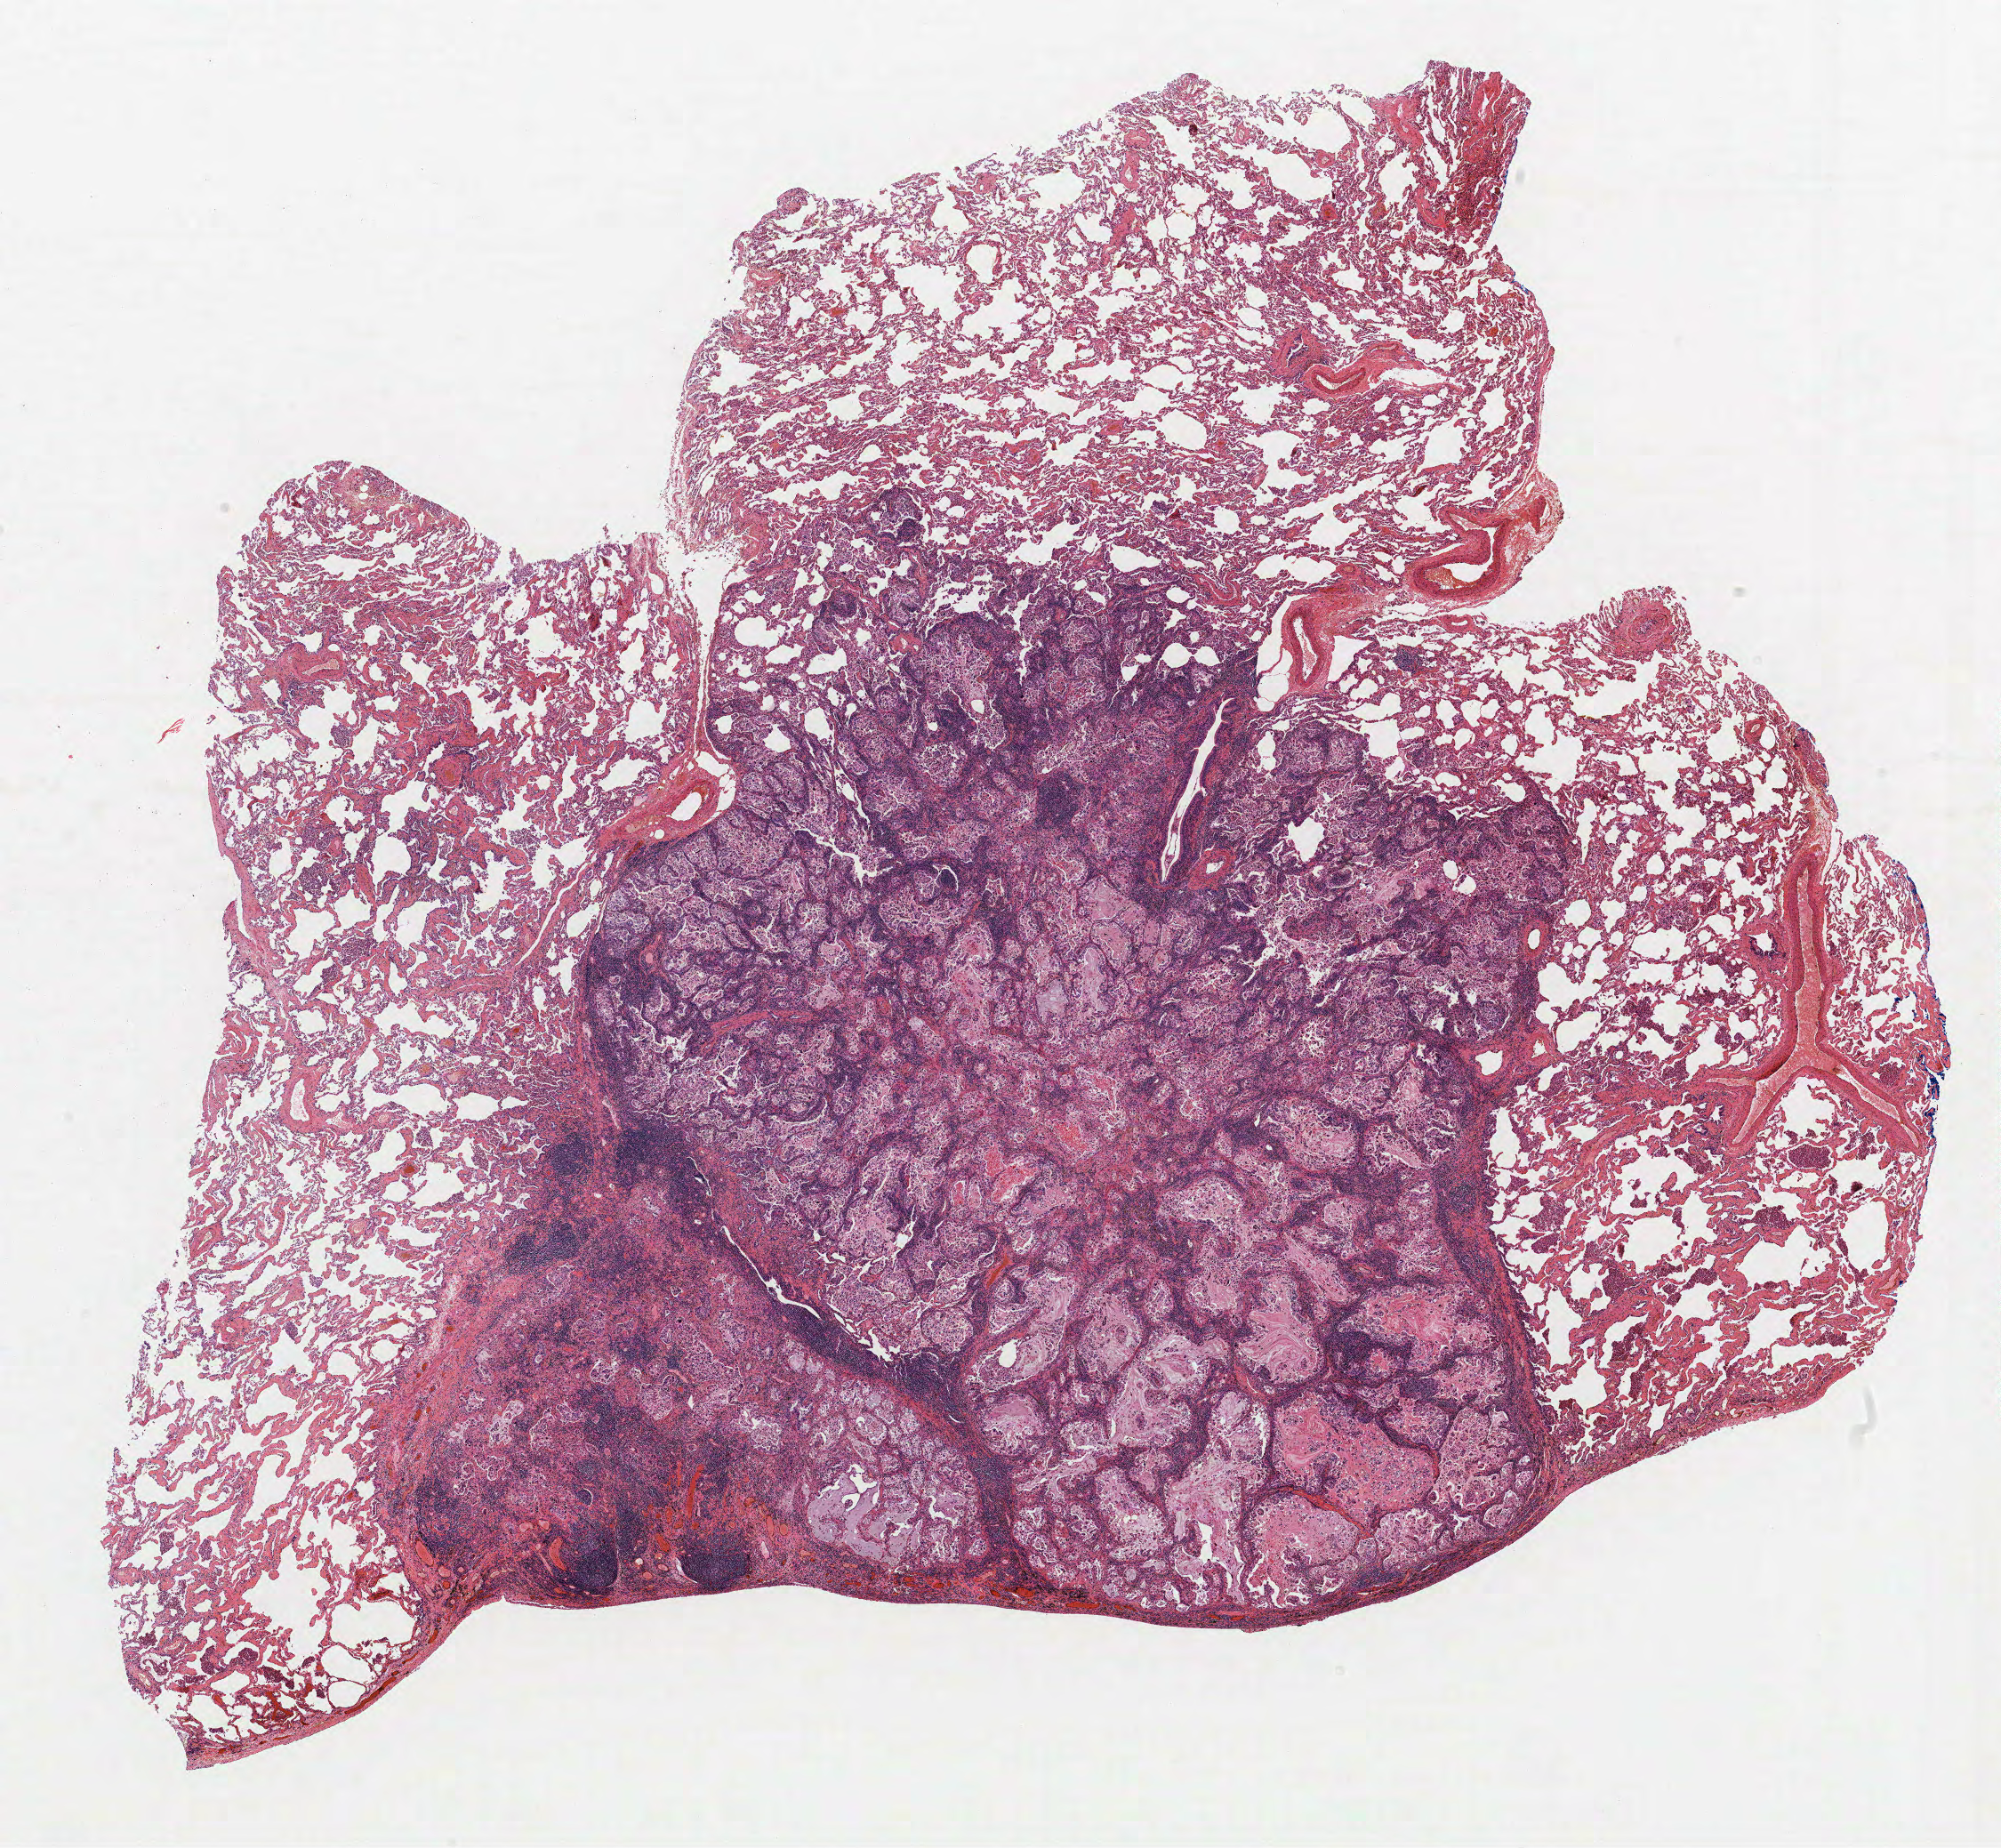
H&E-stained whole-slide image, low-resolution overview of the scanned area, about 18.0 x 16.6 mm; formalin-fixed paraffin-embedded (FFPE) section; lung. Male patient, aged 55 at enrolment. Current smoker at enrolment. Grade: moderately differentiated (G2).
• ICD-O-3 topography: upper lobe of lung (C34.1)
• primary tumour location (clinical record): right upper lobe
• stage (AJCC 6th edition): IIB
• participant's lung-cancer diagnosis: Mucinous adenocarcinoma
• tumour size (pathology): 13 mm